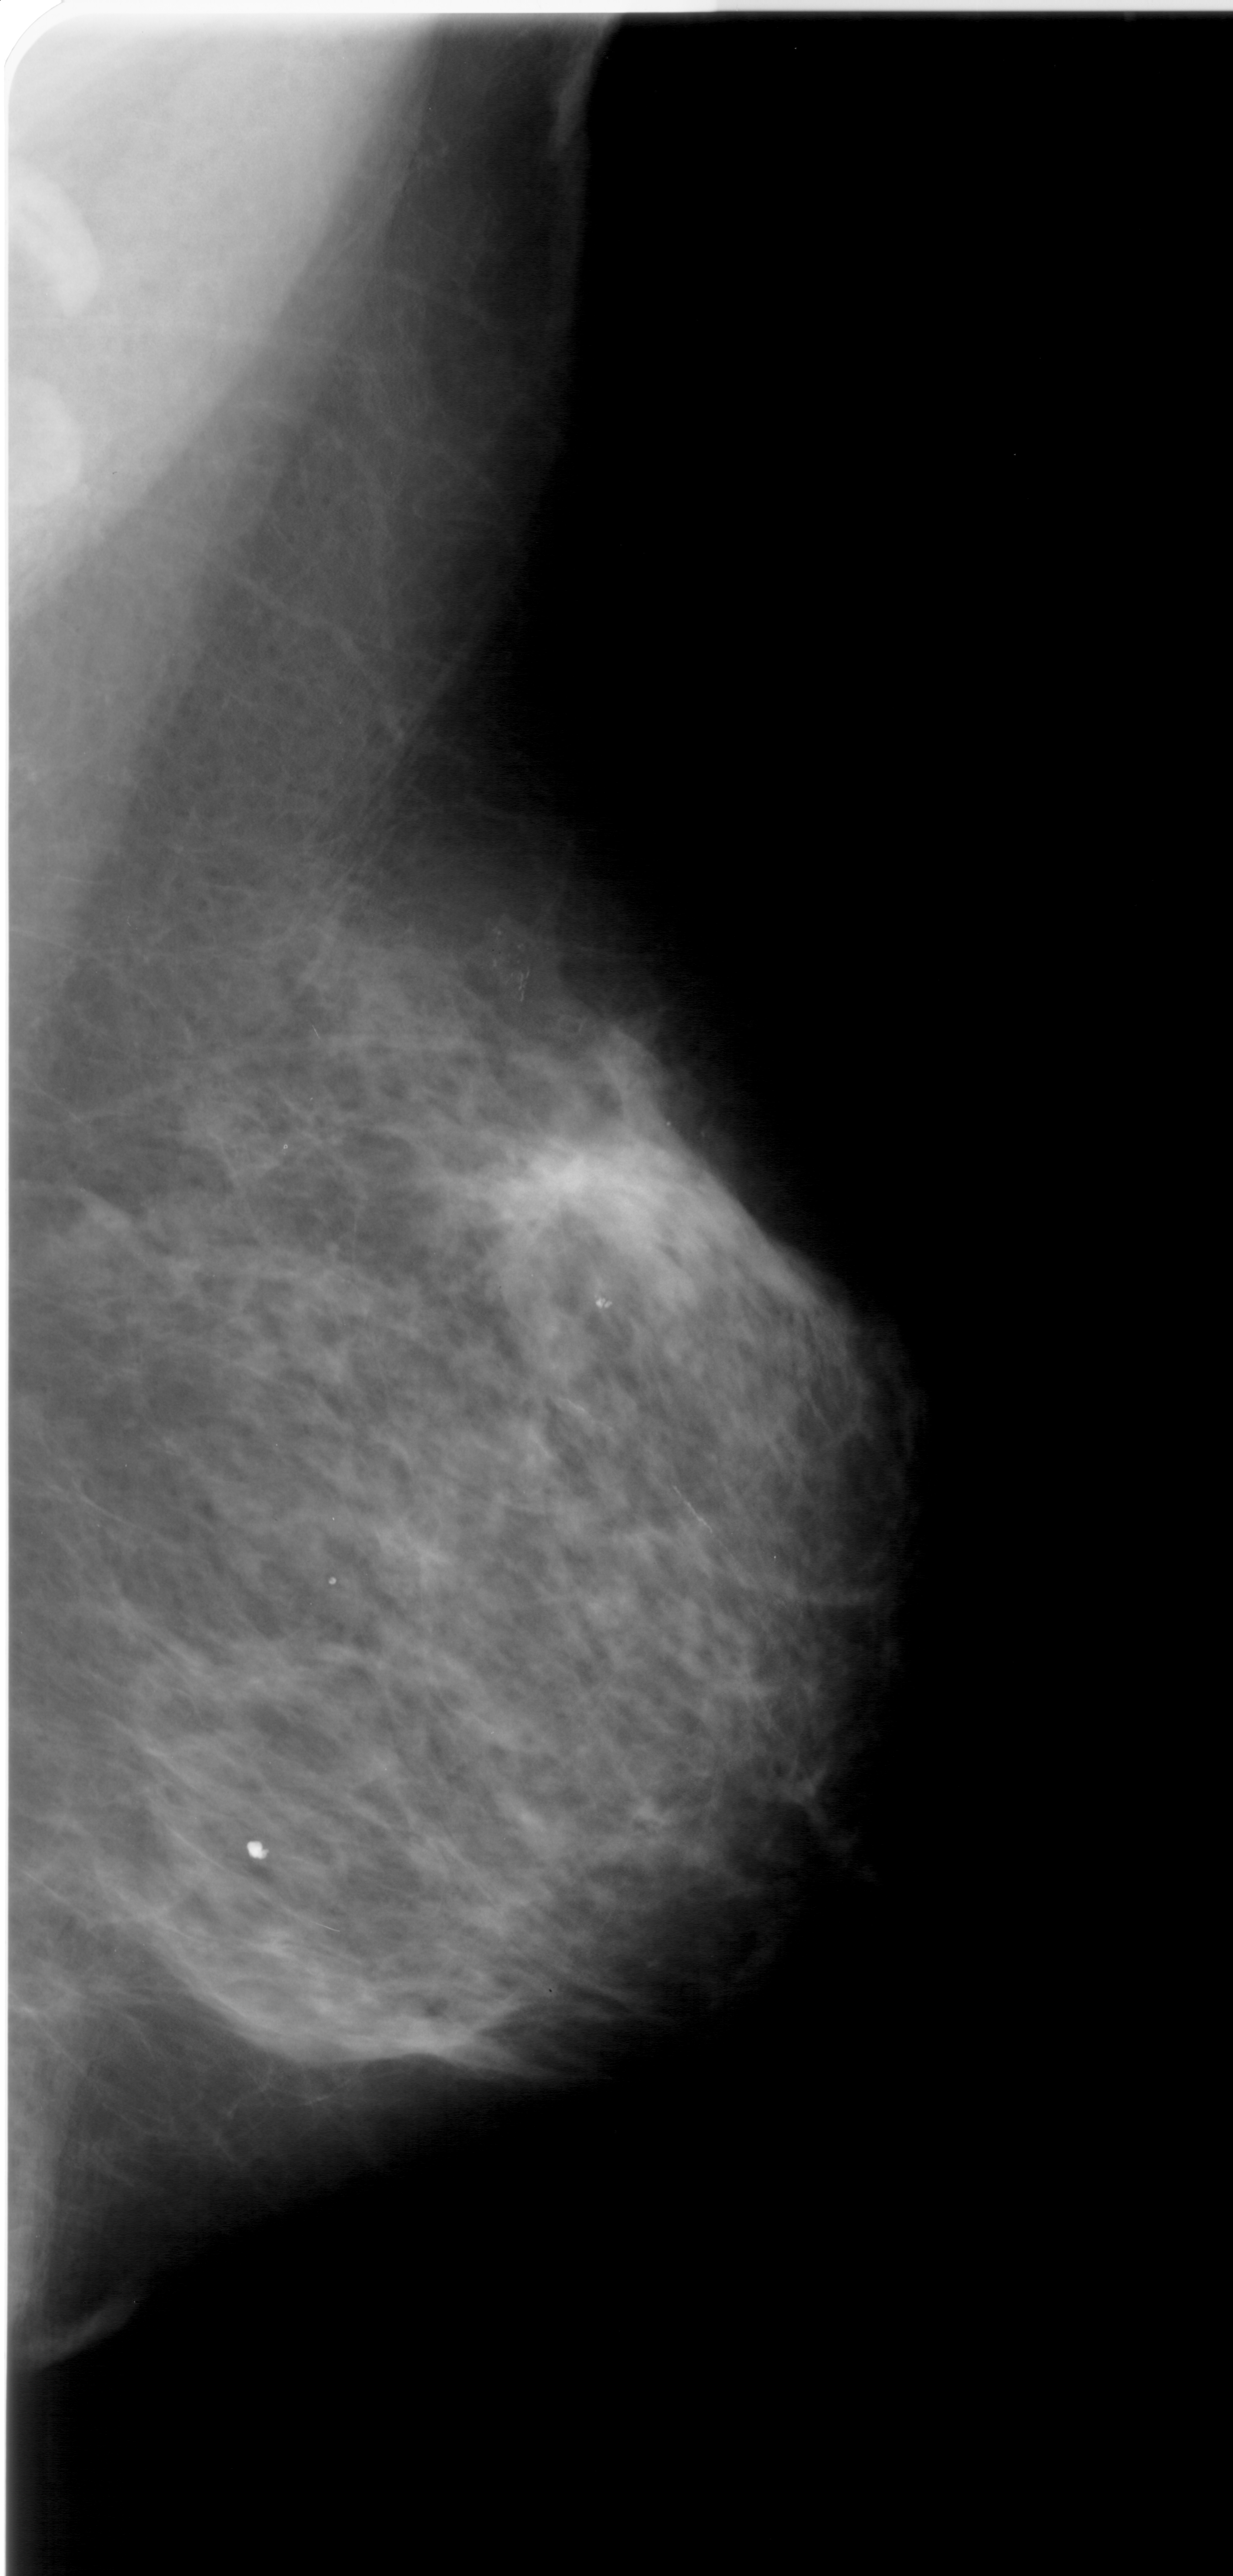
Digitized screen-film mammogram. Right breast. Mediolateral oblique (MLO) view. BI-RADS breast density category 3 (scale 1–4). 1233 × 2576 image matrix.
Marked abnormalities (boxes around the expert regions of interest):
- calcifications, morphology pleomorphic, distribution clustered; BI-RADS assessment category 4; subtlety rating 2 on a 1 (subtle) to 5 (obvious) scale; pathology result (as recorded, not read from the image): benign: bounding box [x1, y1, x2, y2] px = [467, 895, 538, 1001]